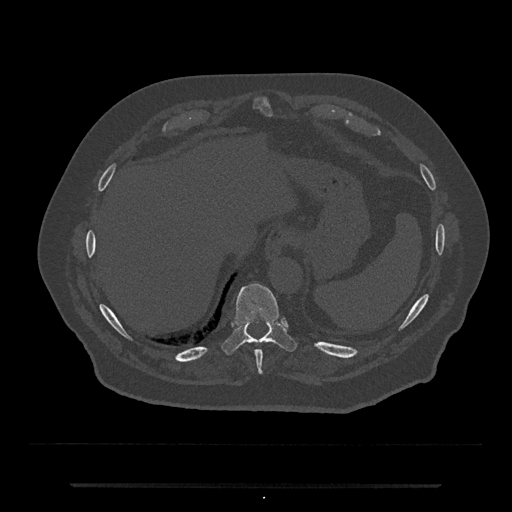
CT including the spine, one axial slice; position 717 of 797 along the scan axis; bone window (W 1800 / L 400 HU); 0.5 mm slice thickness; 512 × 512 image matrix, field of view 434 × 434 mm. Male patient, age 80 years. Case-level facts recorded for this patient, not image findings: primary cancer: prostate.
Structures marked on this image (semi-automatically segmented with operator editing):
- T10 vertebra: bounding box [x1, y1, x2, y2] px = [222, 283, 296, 354]
- T9 vertebra: [255, 350, 263, 374]